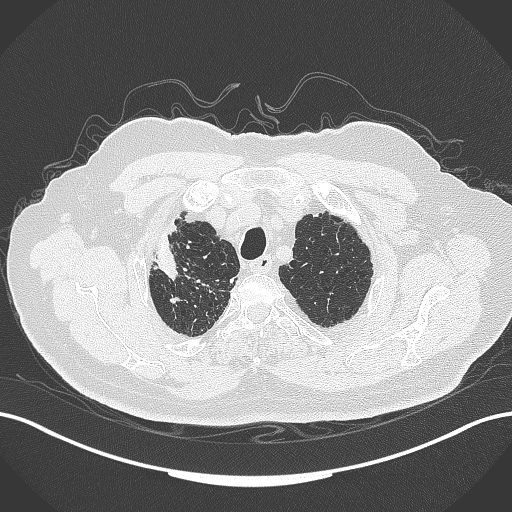
Chest CT, one axial slice; slice 308 of 389 in the series (ordered by position); reconstruction kernel B70f; 120 kVp; lung window (W 1500 / L -600 HU); 1 mm slice thickness; 512 × 512 image matrix, field of view 400 × 400 mm. Male patient, age 72 years. Case-level facts recorded for this patient, not image findings: clinical TNM (as recorded): T1a N0 M0.
Structures marked on this image (rectangle marked by the reading radiologist):
- lung tumour (recorded histology: squamous cell carcinoma): box from (x=153, y=229) to (x=185, y=286) px